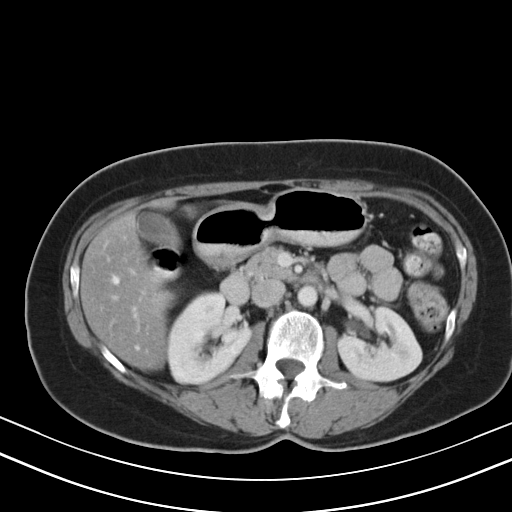
Contrast-enhanced abdominal CT, one axial slice; slice 22 of 47 in the series (ordered by position); intravenous contrast given; soft-tissue window (W 400 / L 40 HU); 512 × 512 image matrix, field of view 350 × 350 mm. Female patient. From the clinical record (not read from this slice): diagnosis: colorectal cancer liver metastases, imaged before liver resection; multiple liver metastases: no; largest metastasis: 3.5 cm.
Outlined on this slice (expert manual segmentation):
- hepatic veins: bounding box [x1, y1, x2, y2] px = [113, 276, 135, 315]
- liver: [81, 218, 165, 368]
- planned liver remnant (the part of the liver to remain after resection): [81, 218, 165, 368]
- portal vein (with intrahepatic branches): [129, 268, 166, 283]